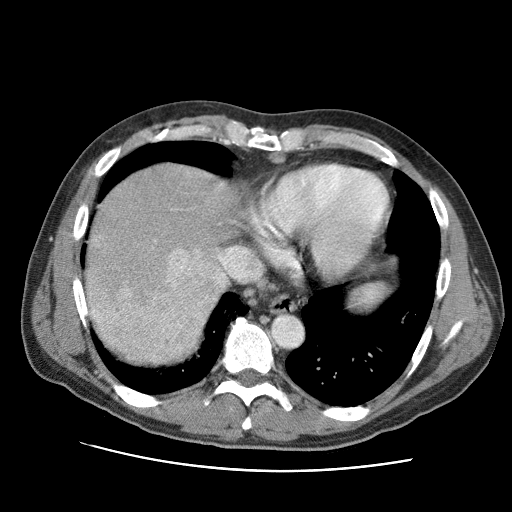
Contrast-enhanced abdominal CT (liver protocol), one axial slice. Slice 83 of 95 in the series (ordered by position). Reconstruction kernel STANDARD. One of 2 acquisitions stored at this slice position. Soft-tissue window (W 400 / L 40 HU). 2.5 mm slice thickness. 512 × 512 image matrix, field of view 360 × 360 mm. Case-level facts recorded for this patient, not image findings: diagnosis: hepatocellular carcinoma (patient treated with transarterial chemoembolisation; whether this scan precedes or follows treatment is not stated here); TNM stage (as recorded): Stage-IVA; Child-Pugh class: A; tumour differentiation: moderately differentiated; tumour nodularity: multinodular.
Annotated regions visible in this slice (semi-automatic segmentation, software-assisted and operator-edited):
- liver parenchyma outside the tumour (the mass and vessels are separate outlines, so this box may not span the whole liver): bounding box <86,164,263,327> (left, top, right, bottom; pixels)
- mass: <85,233,217,364>
- liver vessels: <195,249,261,280>